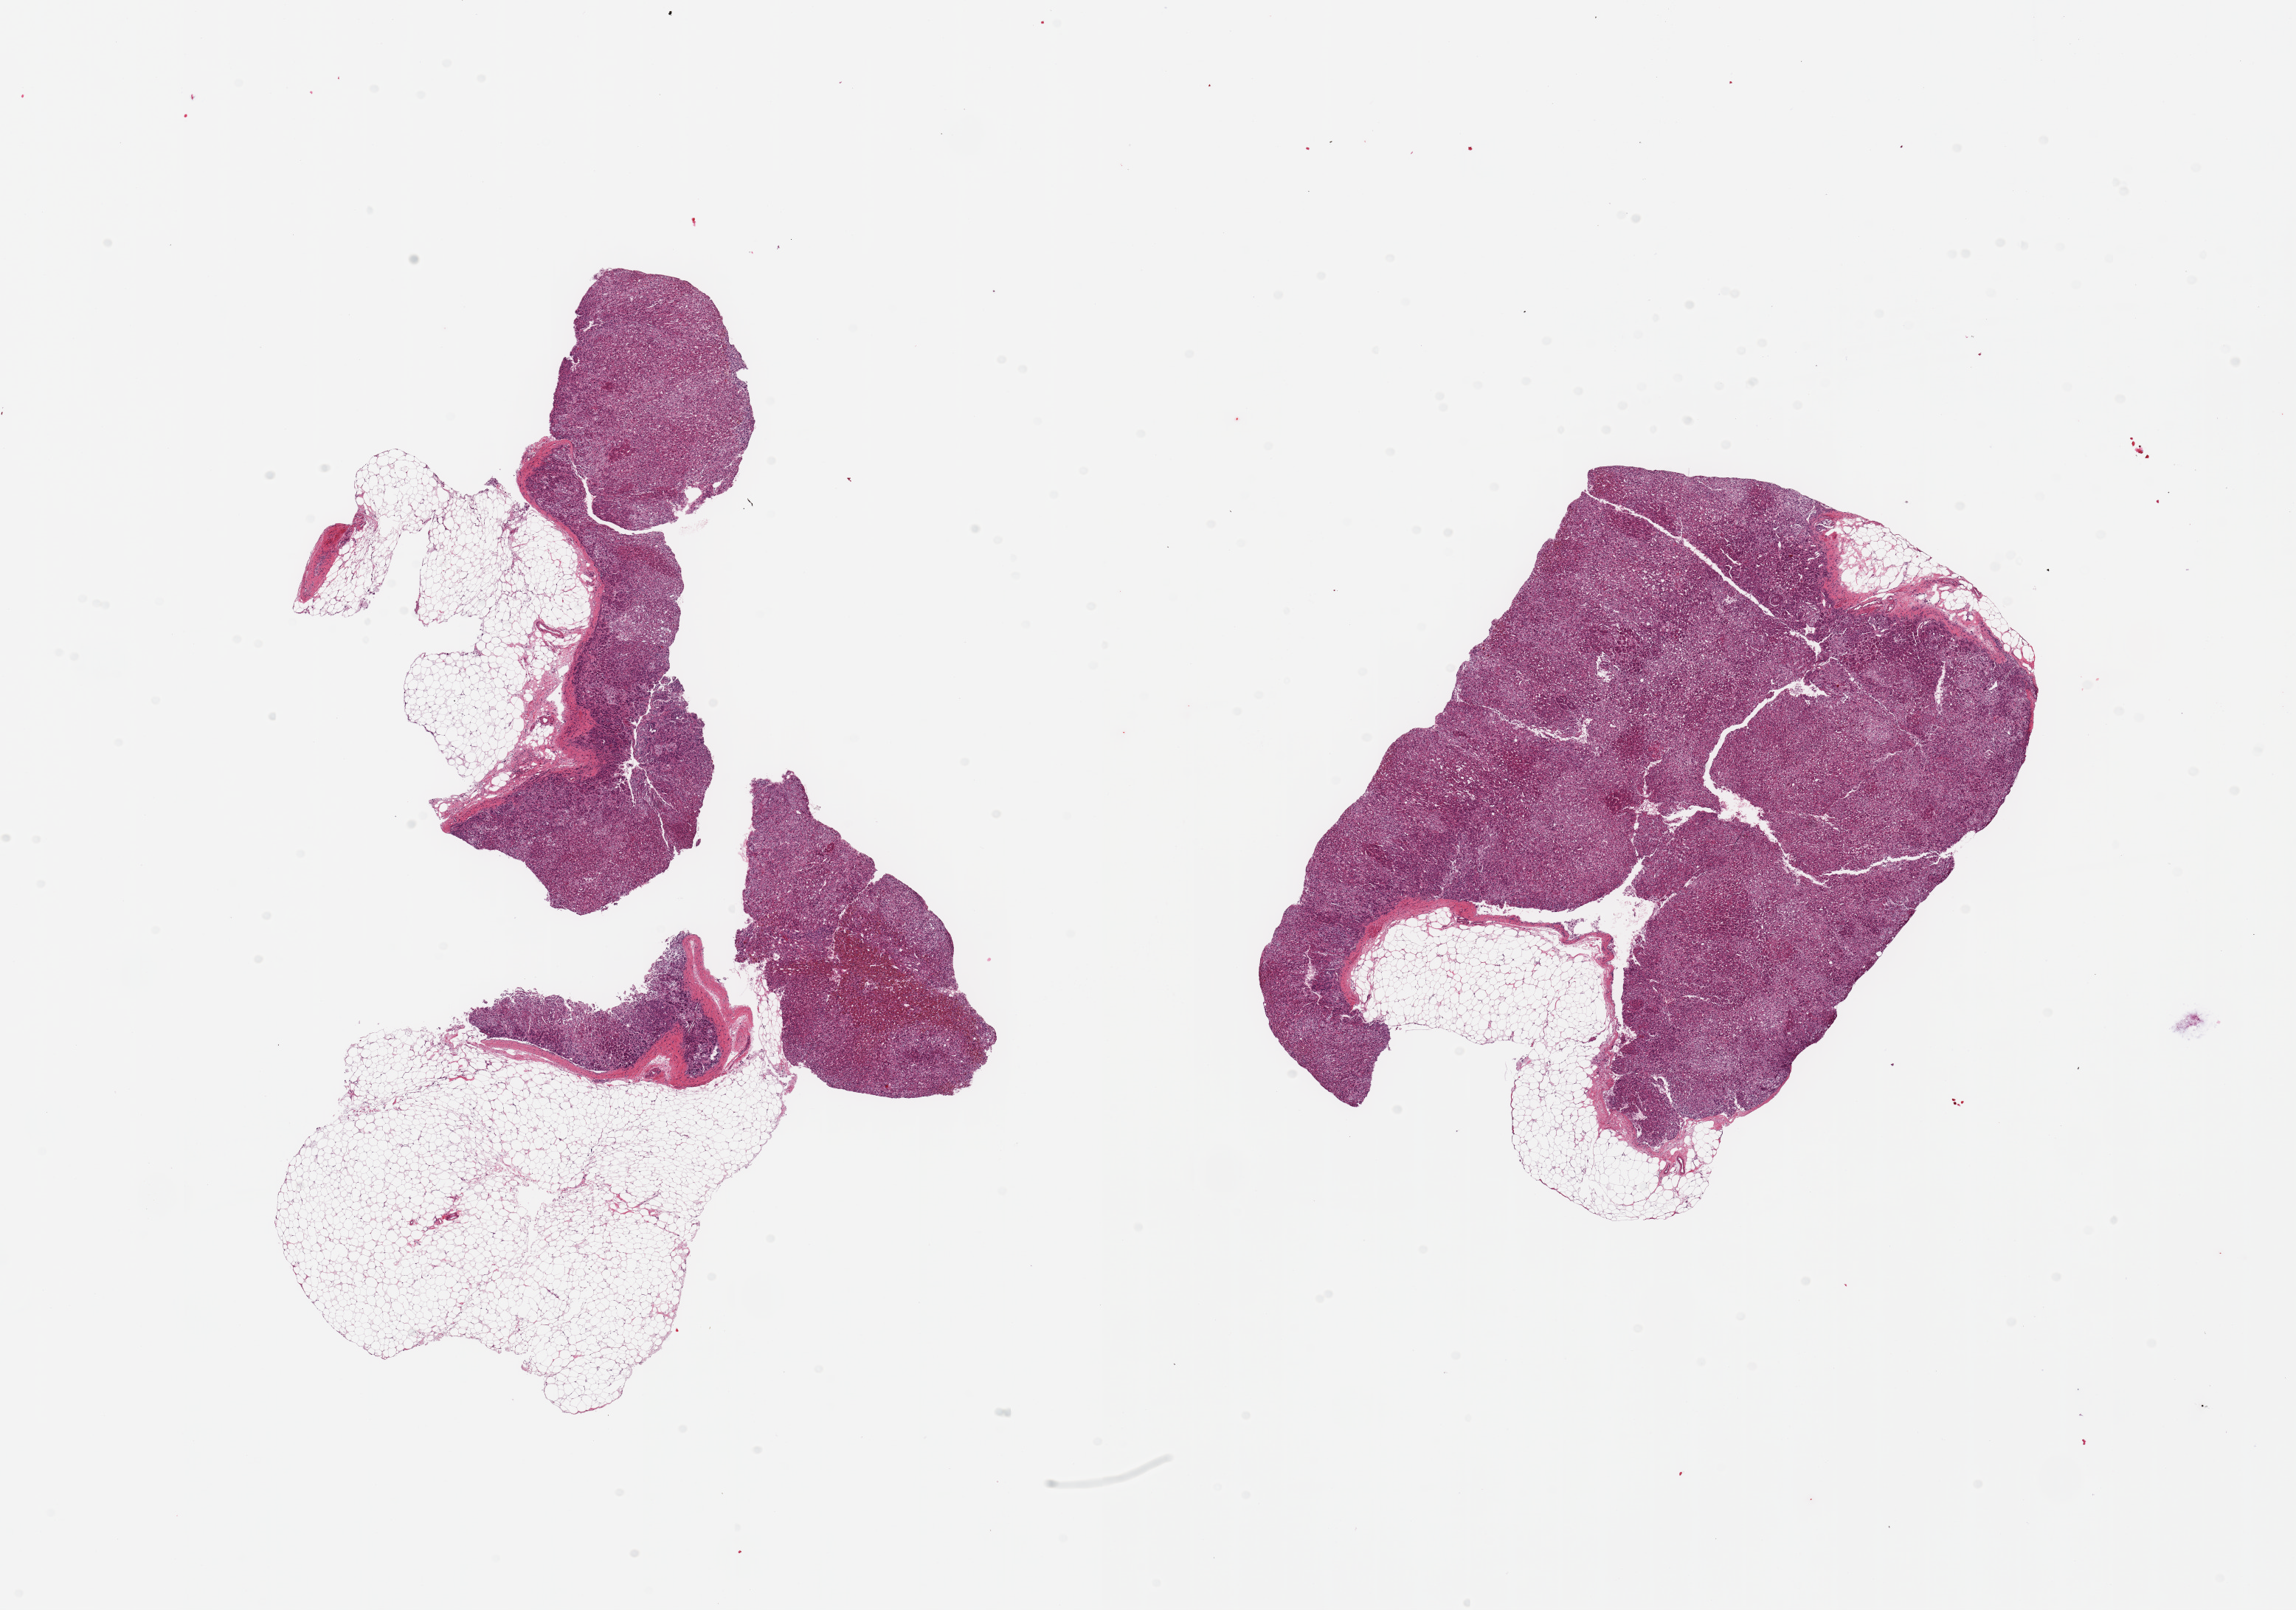
Digitized hematoxylin and eosin (H&E)-stained section, brightfield — low-resolution overview of the scanned area, about 24.6 x 17.3 mm, PAXgene-fixed, paraffin-embedded tissue, target tissue: adrenal gland, tissue donor sample.
Pathologist's review note for this sample: 2 pieces; 60% & 30% external untrimmed fat.